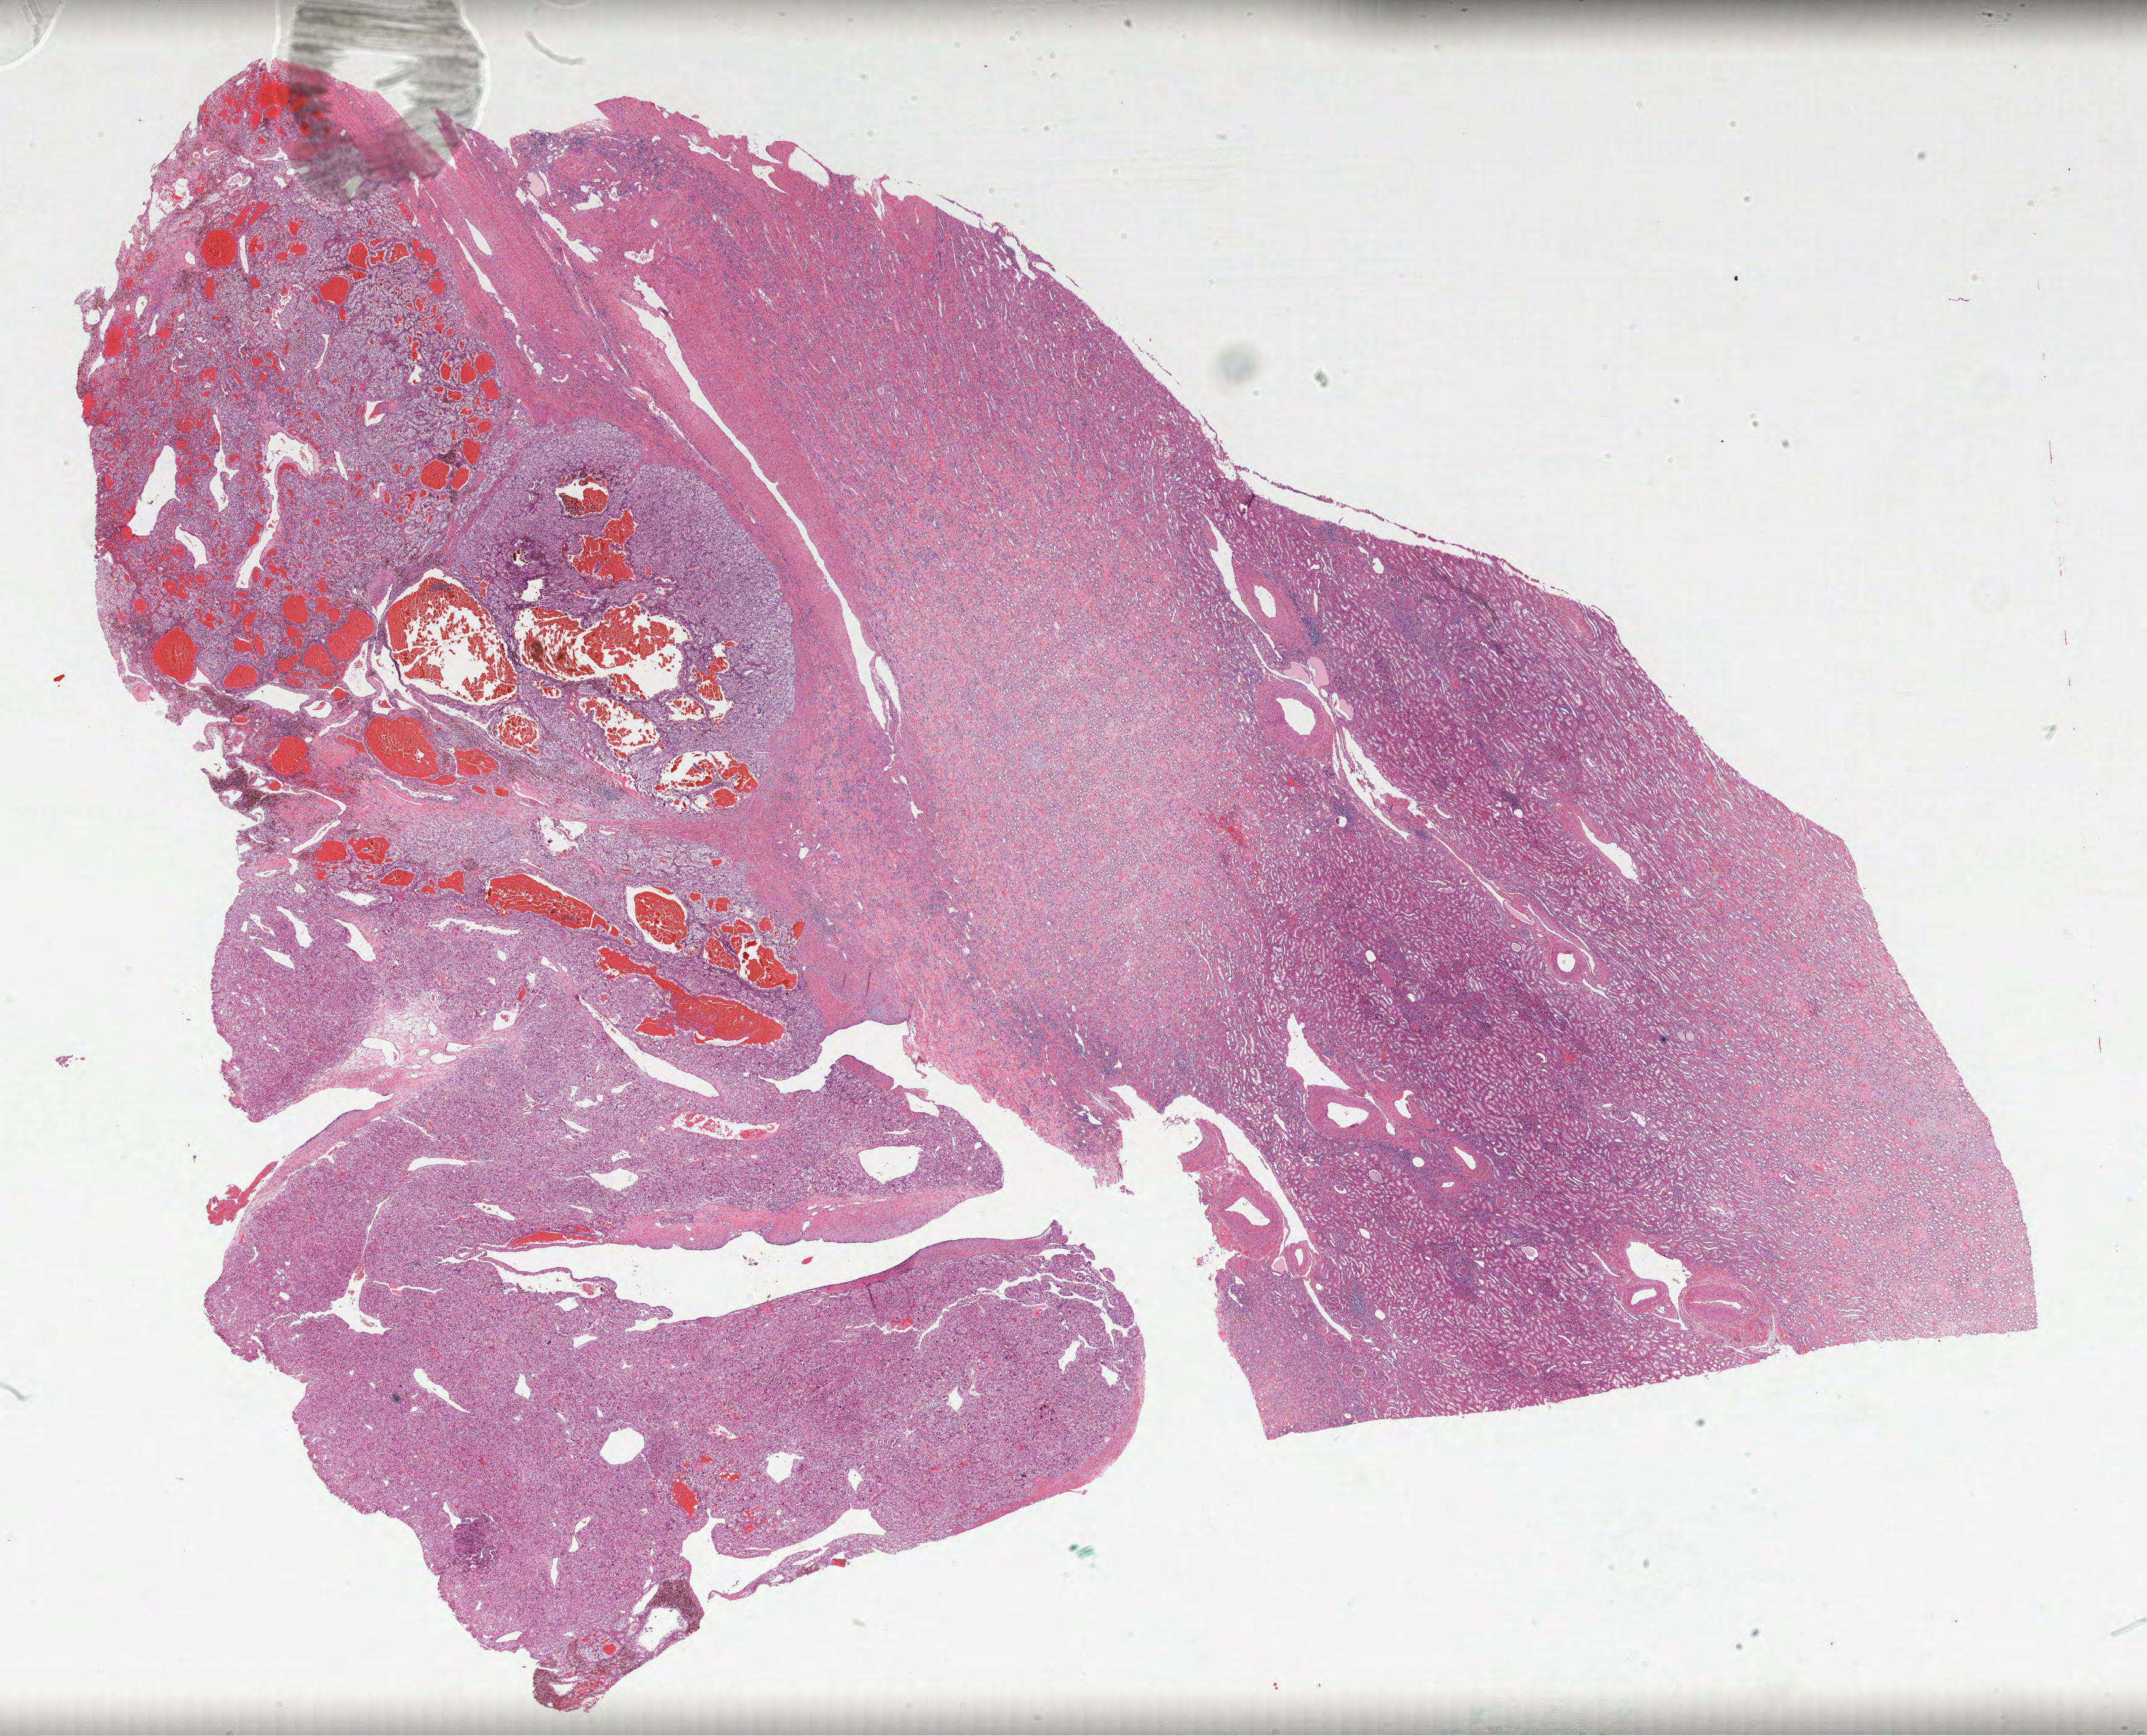
Whole-slide histology image, H&E-stained — shown as a low-resolution overview of the whole scanned area (about 28.3 x 22.9 mm, from a 40x scan), FFPE section, sample: primary tumour, kidney. Male patient; age at initial diagnosis 62 years. Histologic grade: G4 (undifferentiated).
Diagnosis: Clear cell adenocarcinoma, NOS. AJCC pathologic stage: III (6th edition). TNM: T3a NX M0.